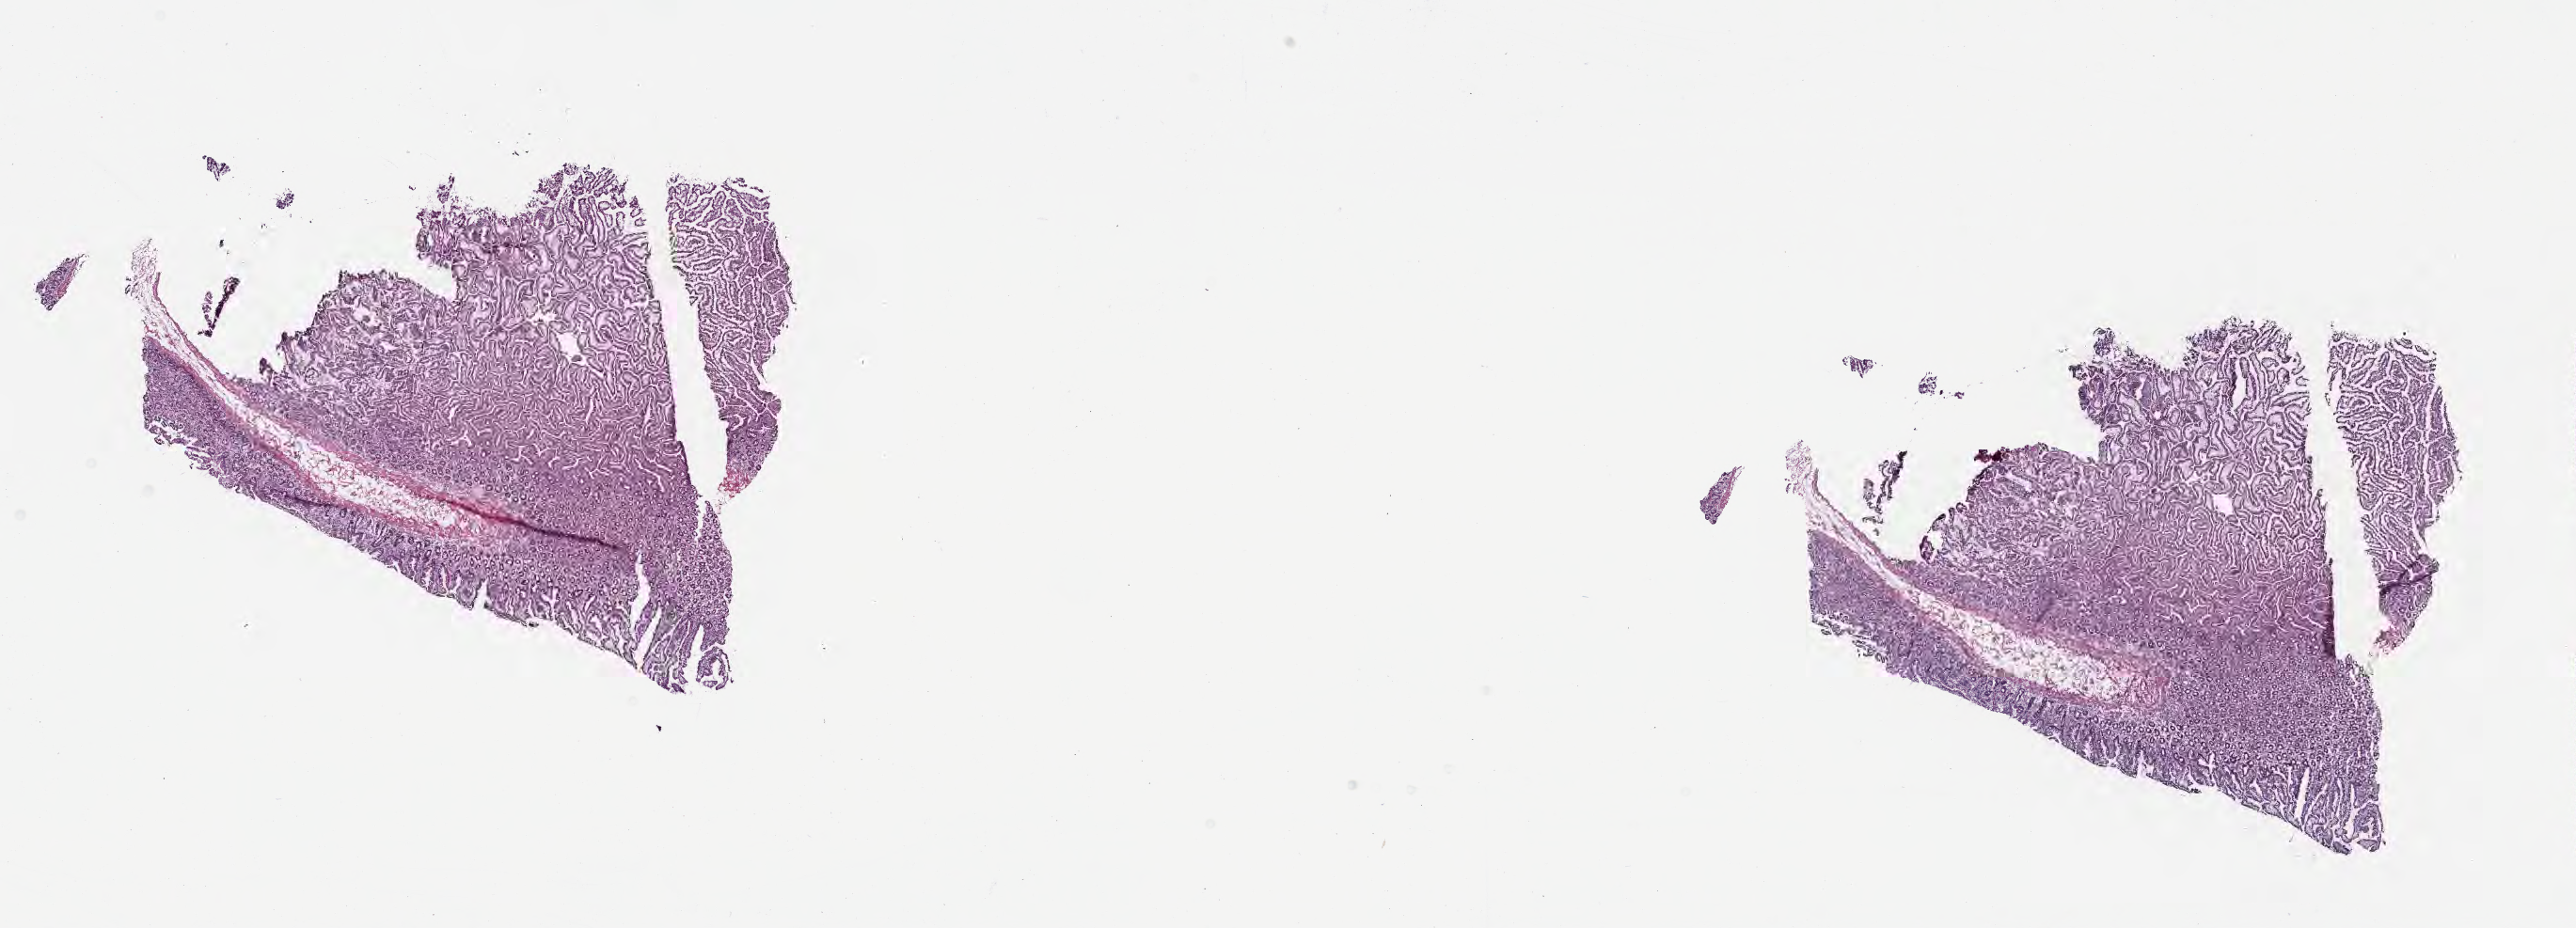
Whole-slide image, H&E stain, whole scanned area (about 22.1 x 8.0 mm) shown as a low-resolution overview; frozen section; normal-tissue sample (non-tumor) from a patient with infiltrating duct carcinoma, NOS; site: head of pancreas. Male patient; age at initial diagnosis 69 years. Slide review estimates, as recorded: tumor cells 0%, tumor nuclei 0%, stromal cells 25%, necrosis 0%, normal cells 75%. Infiltration values recorded for this section: lymphocyte infiltration 6%, monocyte infiltration 3%, neutrophil infiltration 6%.
• this section: non-tumor tissue sample; the patient's diagnosis is given above
• section: top of the tissue portion